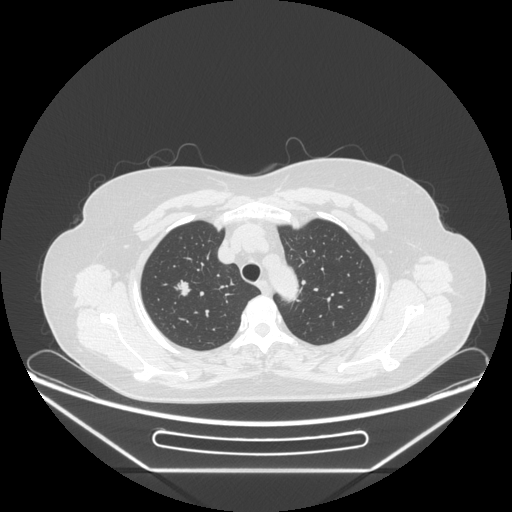
Chest CT, one axial slice. Slice 196 of 236 in the series (ordered by position). Lung window (W 1500 / L -600 HU). 1.25 mm slice thickness. 512 × 512 image matrix, field of view 433 × 433 mm. Patient: female, 60 years. Case-level facts recorded for this patient, not image findings: clinical TNM (as recorded): T1c N0 M0.
Annotated regions visible in this slice (bounding box drawn by a radiologist):
- lung tumour (recorded histology: adenocarcinoma): box from (x=174, y=275) to (x=193, y=302) px